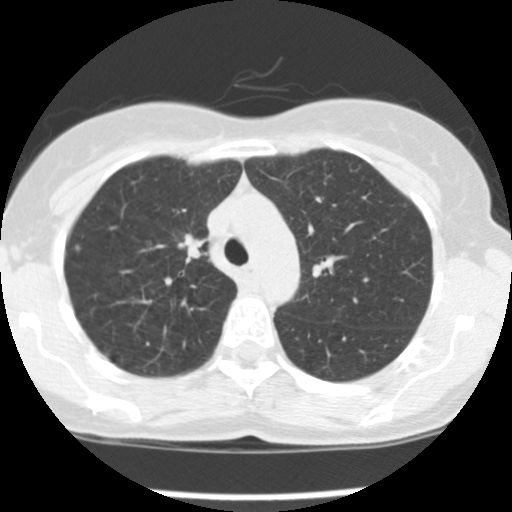
Low-dose screening chest CT, one axial slice. Position 113 of 157 along the scan axis. Lung window (W 1500 / L -600 HU). 512 × 512 image matrix, field of view 282 × 282 mm.
Outlined on this slice (manually delineated by an expert):
- lesion 1 (tumor, upper lobe of right lung): box from (x=178, y=234) to (x=206, y=261) px